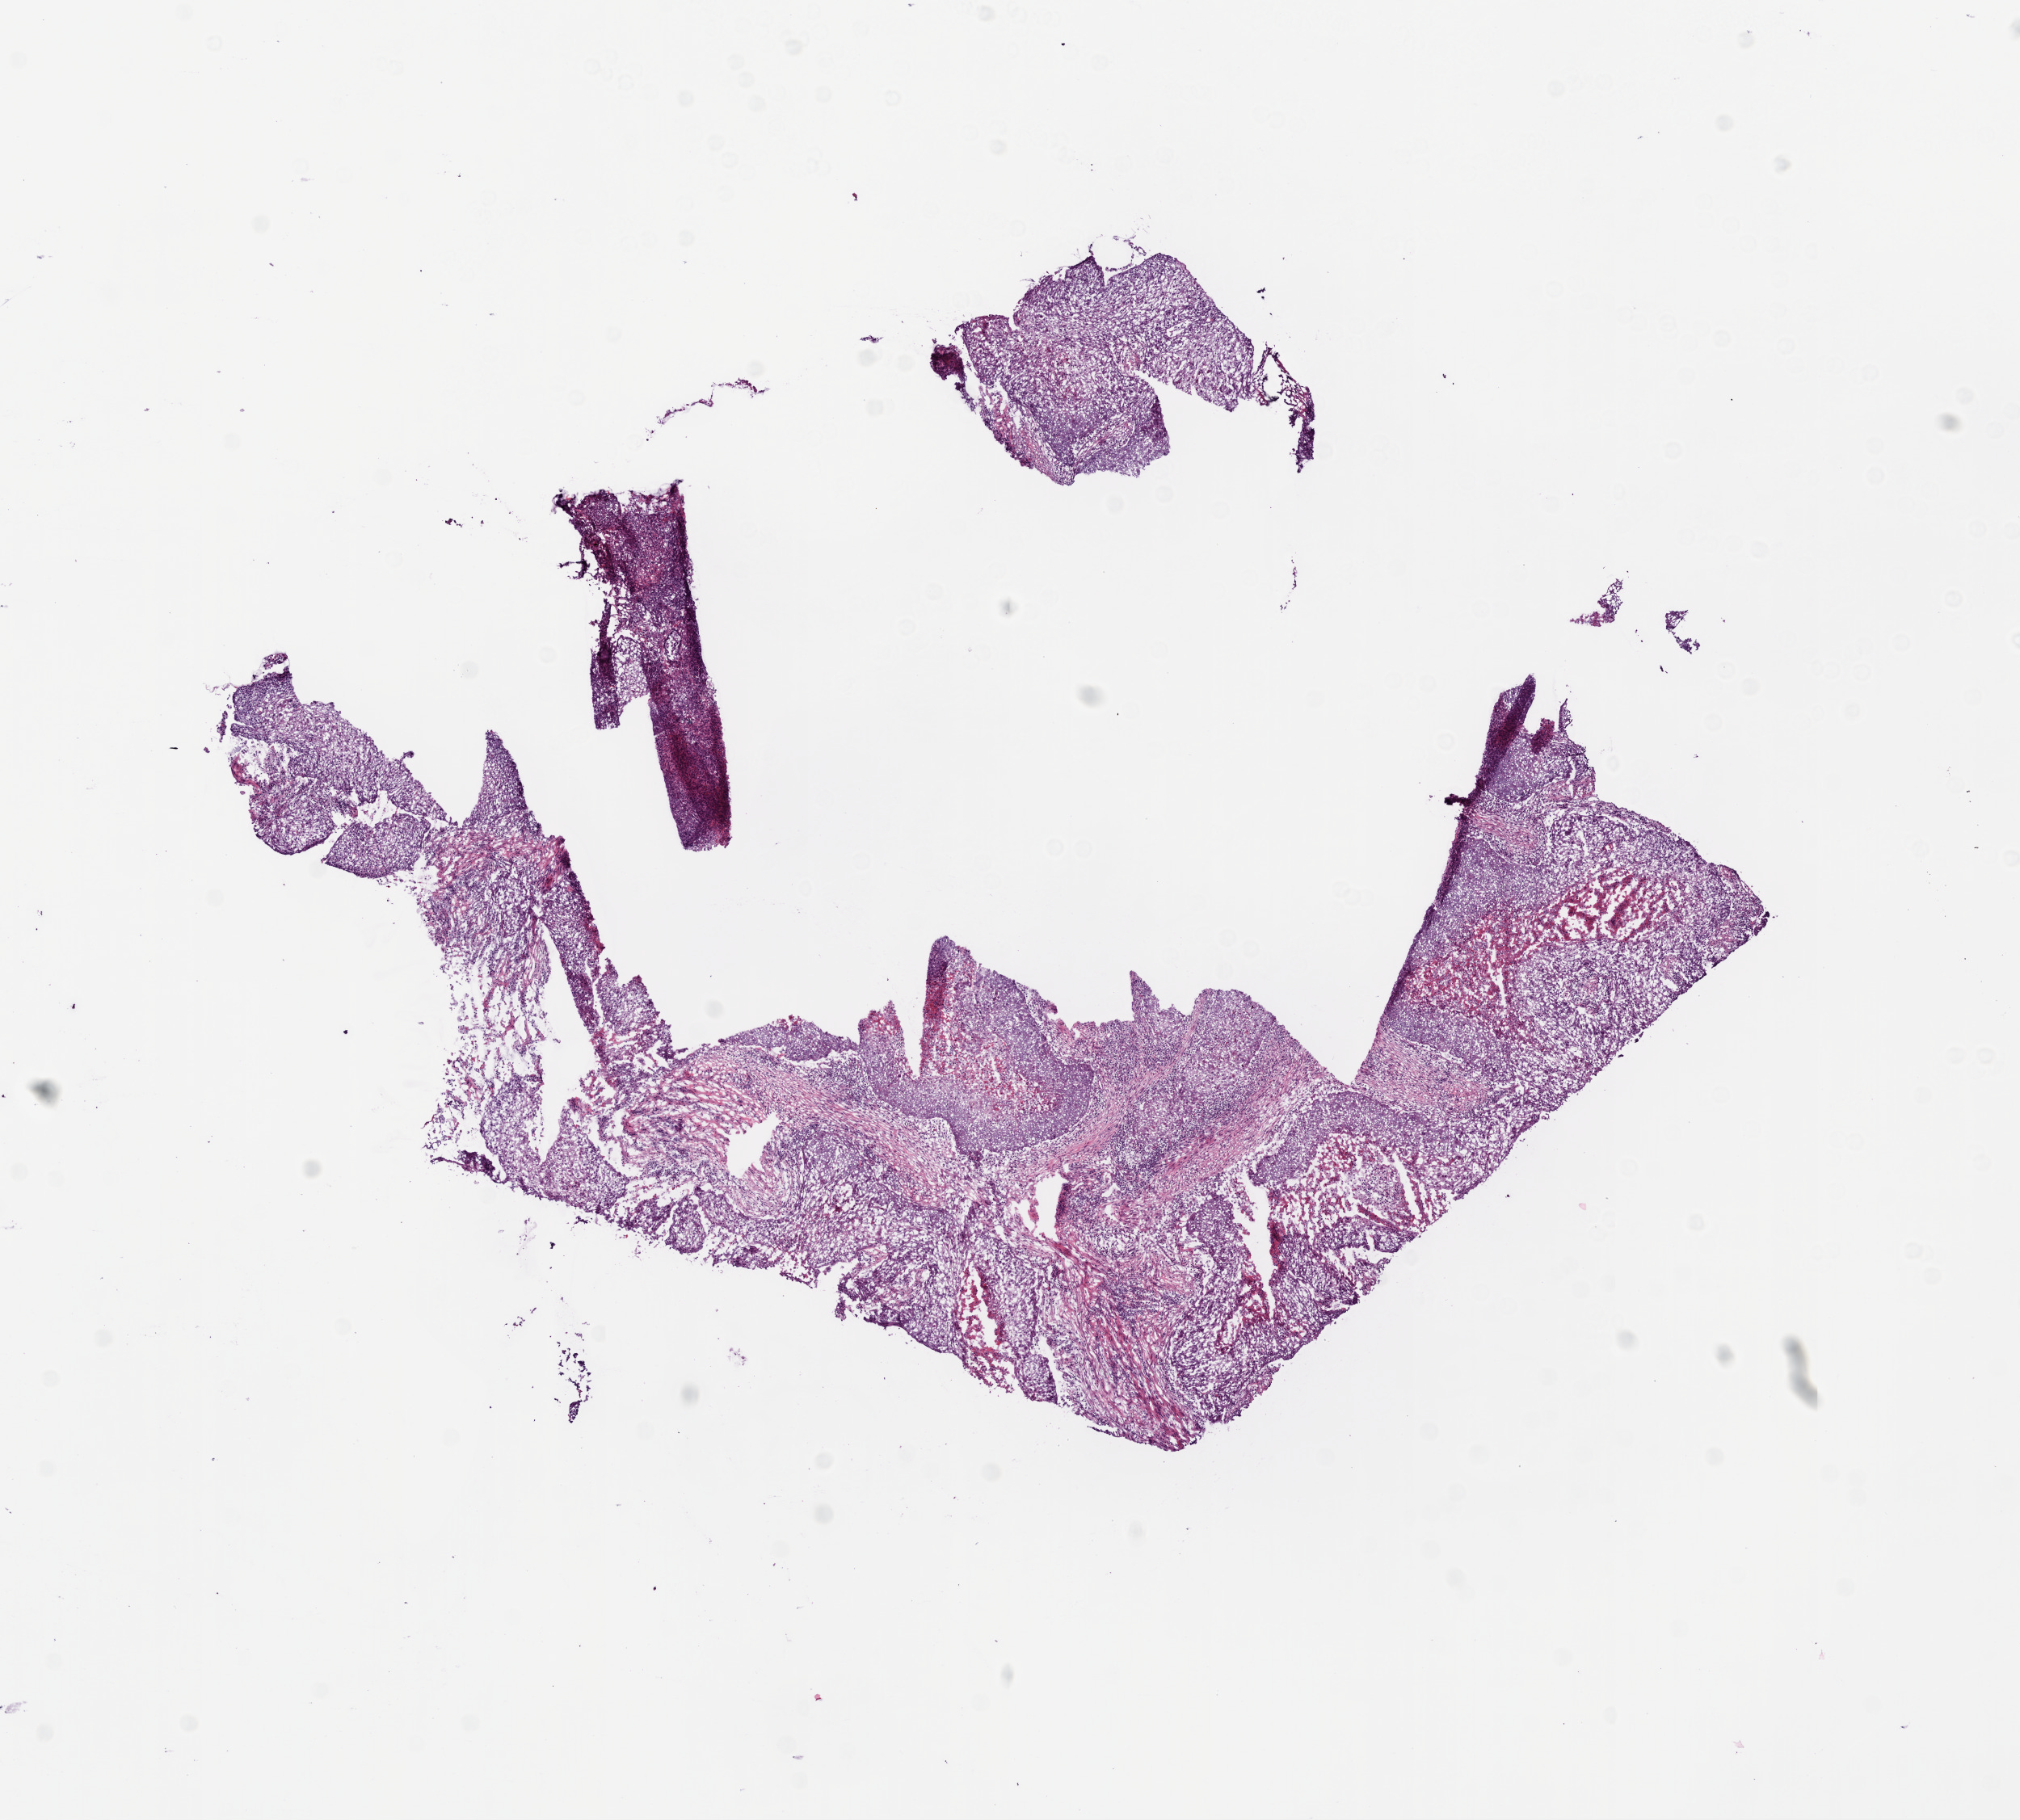
Whole-slide histology image, H&E, whole scanned area (about 10.0 x 9.0 mm, slide scanned at 20x) shown as a low-resolution overview, frozen section from the bottom of the tissue portion, primary tumour sample from the lung. Male, age 51 years at initial diagnosis.
Diagnosis: Squamous cell carcinoma, NOS (upper lobe, lung).